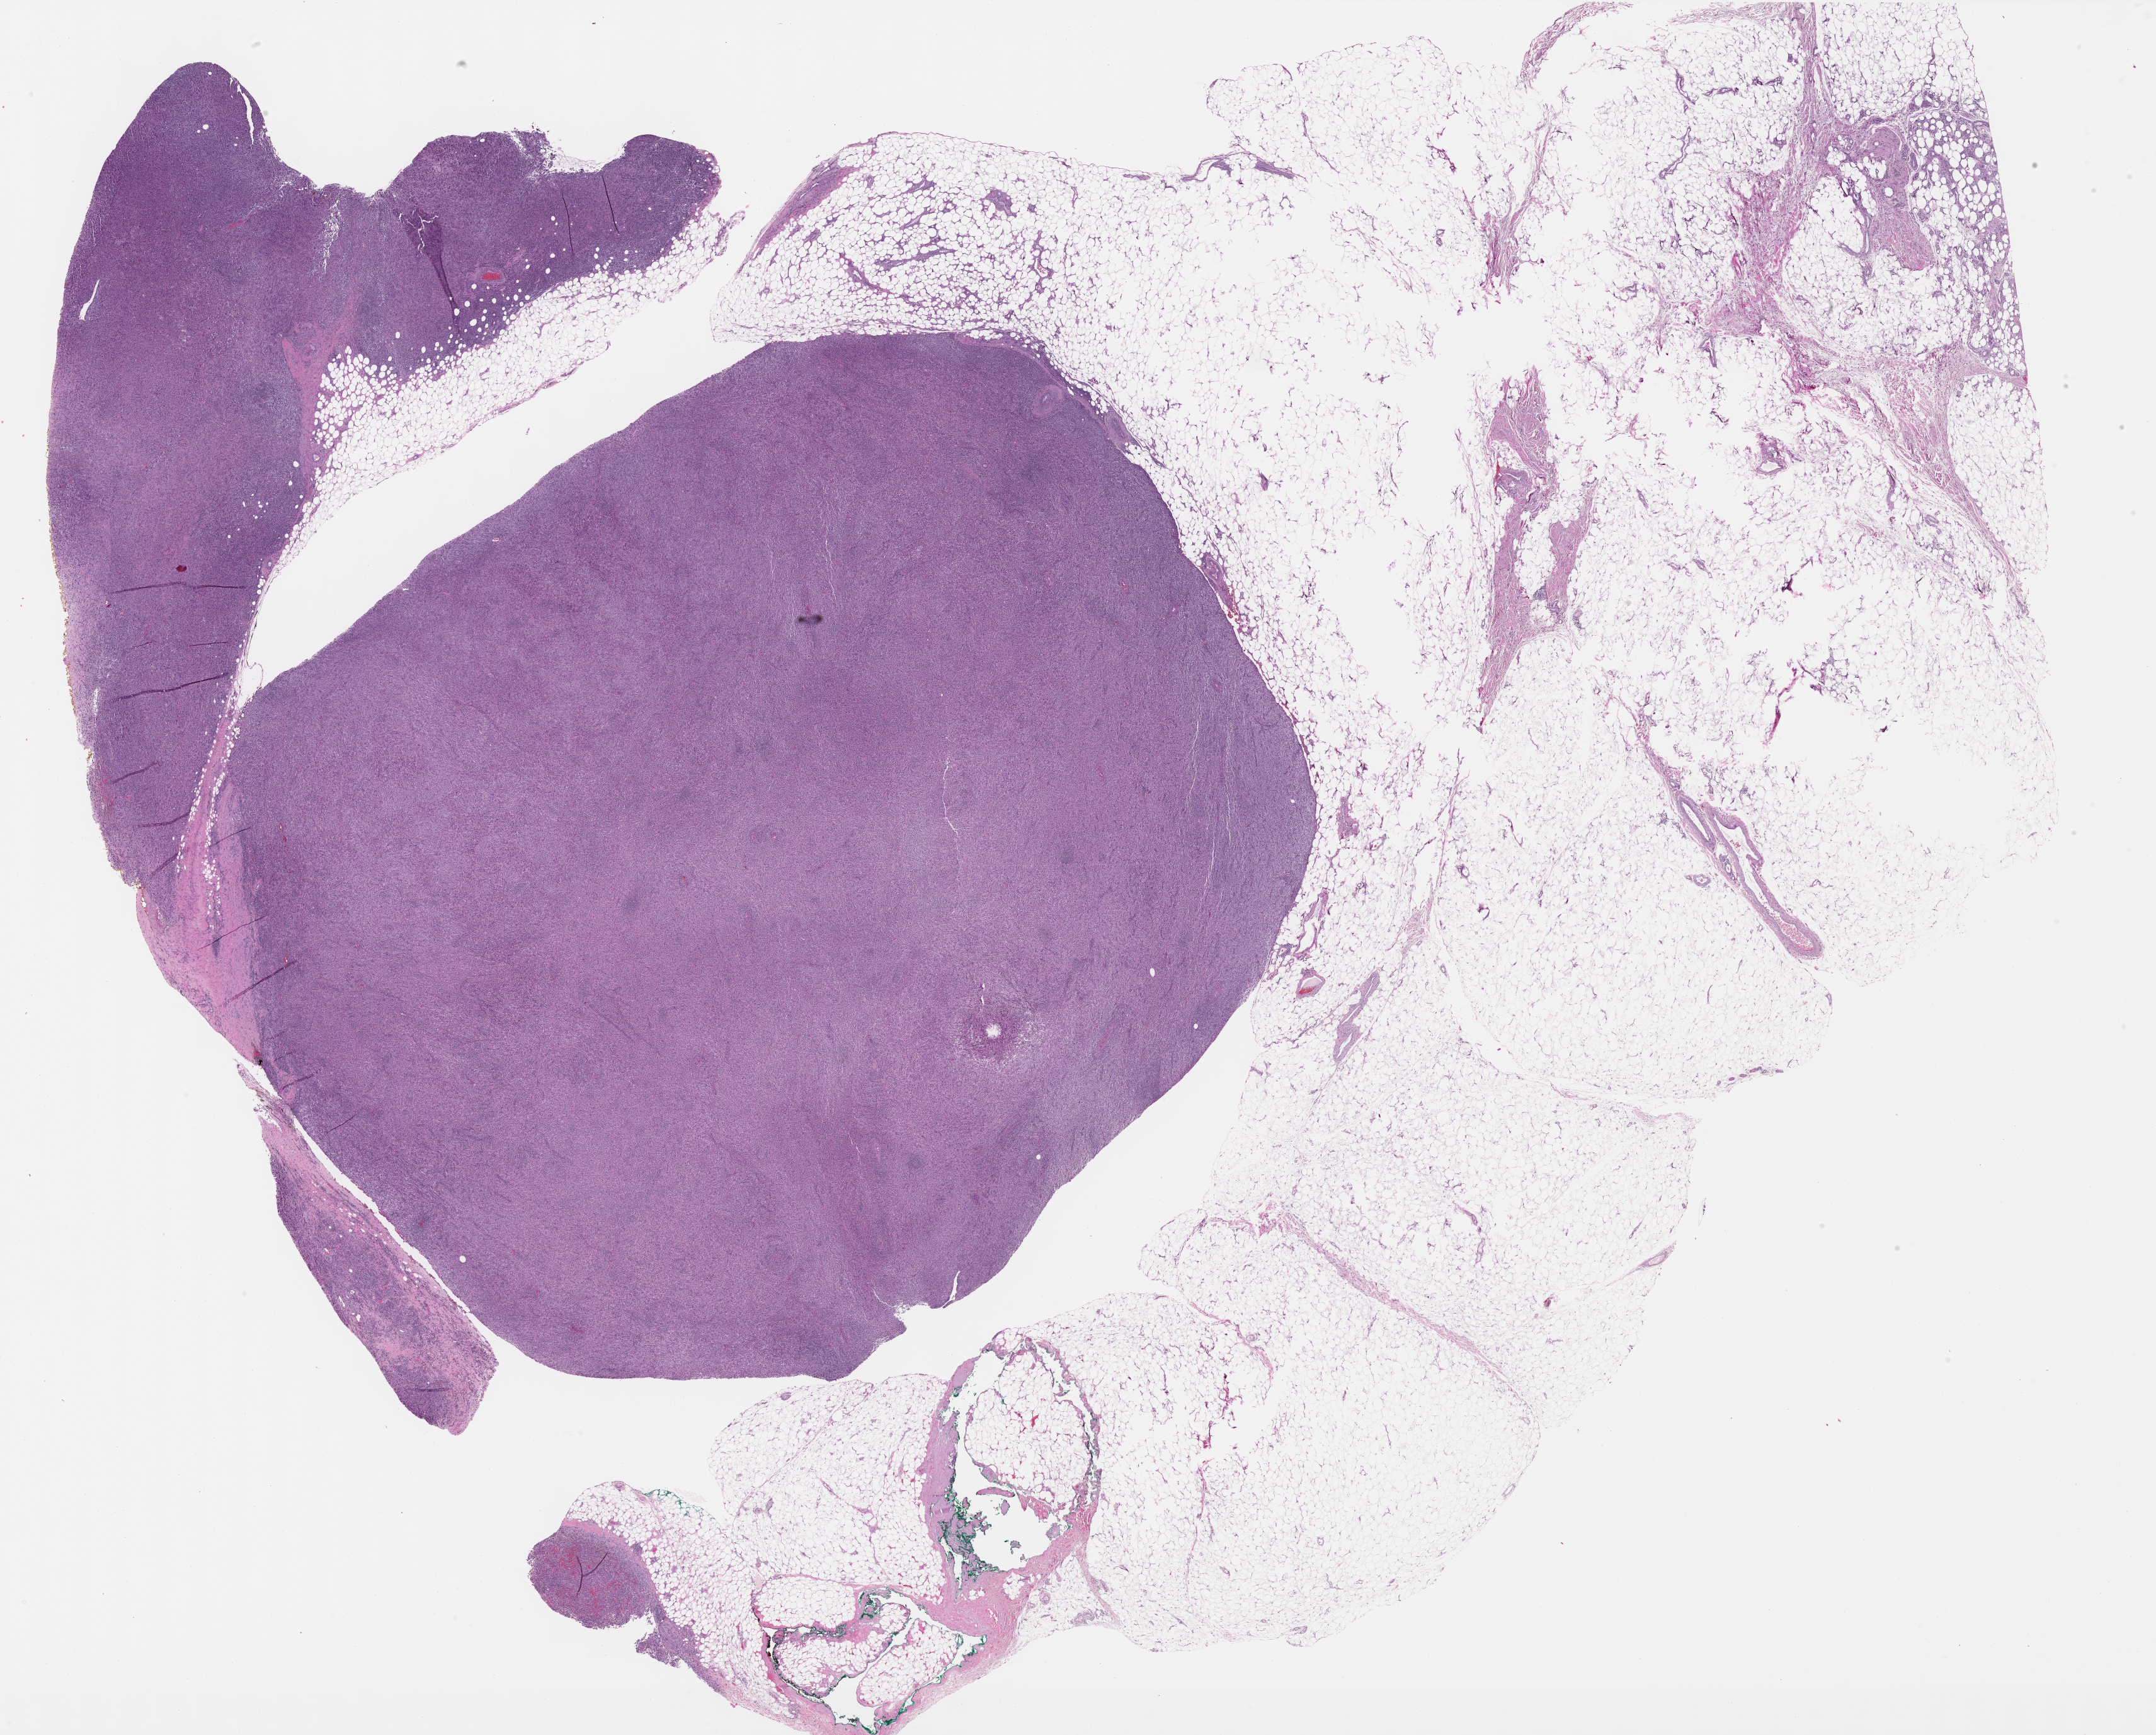
H&E whole-slide image — a low-resolution overview of the entire scanned area, about 27.5 x 22.1 mm (slide scanned at 40x). FFPE section. Sample: primary tumour, connective, subcutaneous and other soft tissues. Male patient; age at initial diagnosis 63 years.
- histologic diagnosis: Malignant fibrous histiocytoma (connective, subcutaneous and other soft tissues of lower limb and hip)